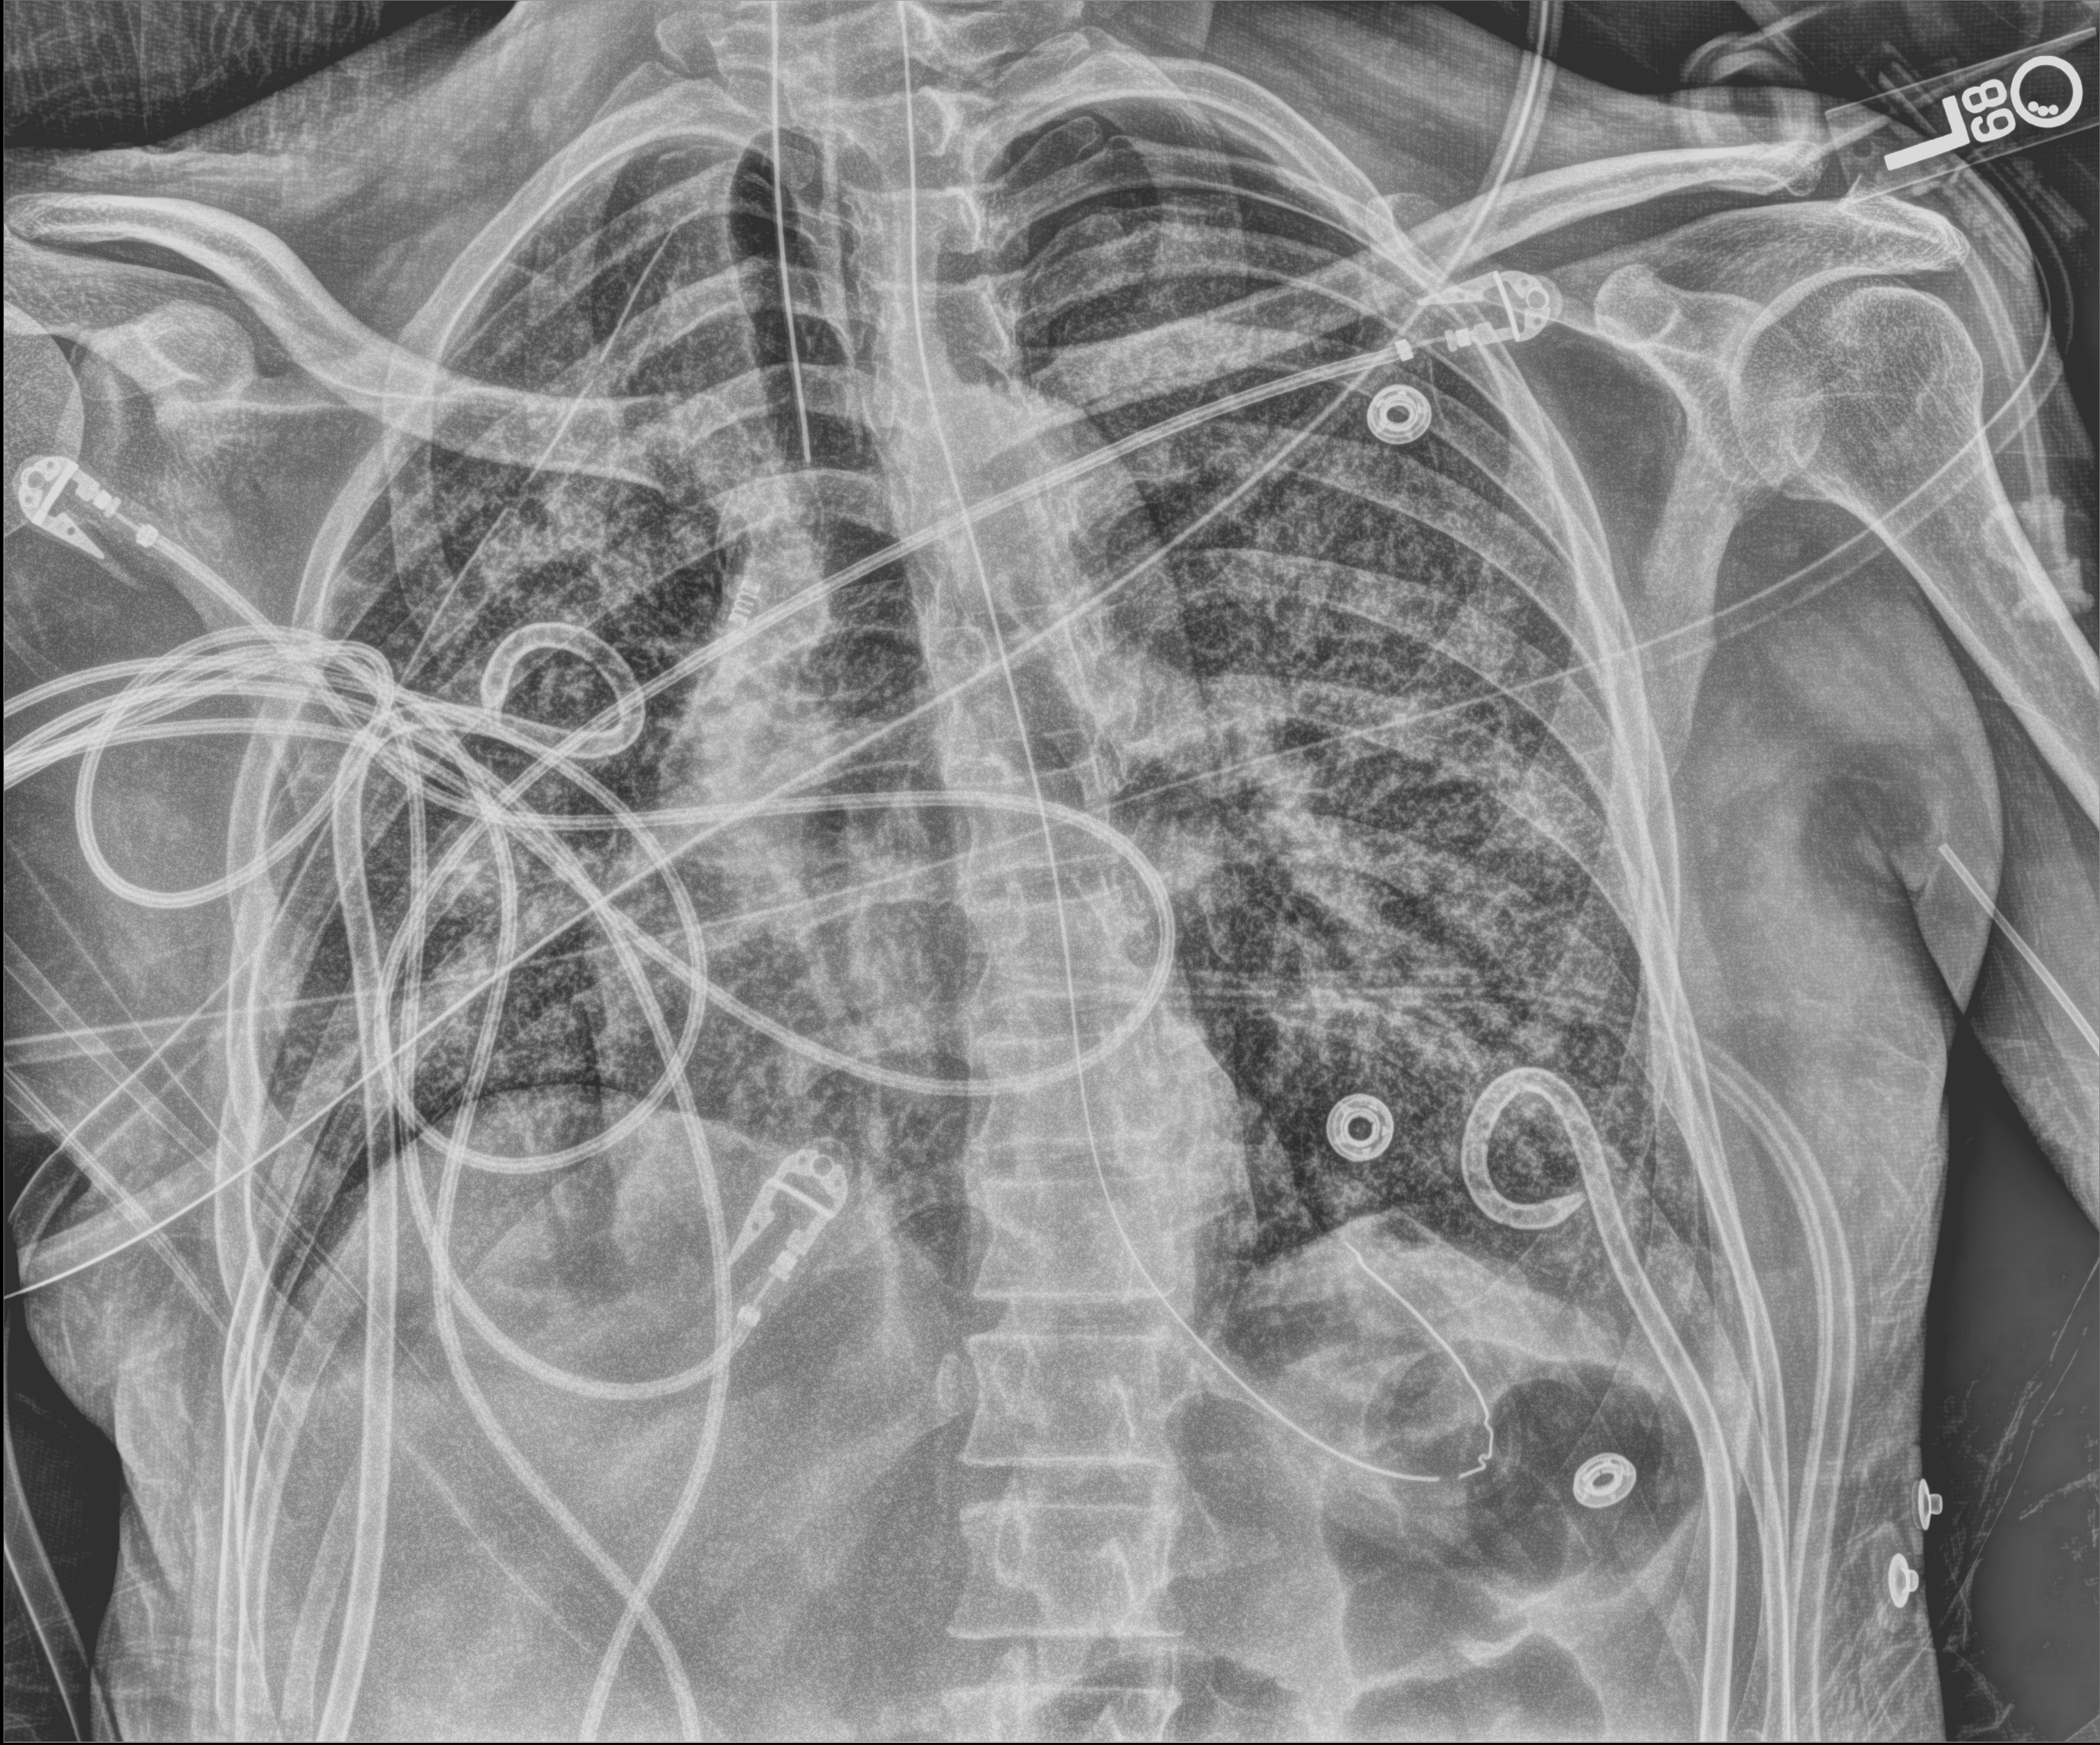
Chest X-ray (portable); anteroposterior (AP) projection. Patient hospitalised with COVID-19, aged 18–59 years.
From the hospital-stay record, not from the radiograph (when in the stay this image was taken is not recorded):
- hypertension (admission record): no
- admitted to intensive care during this hospital stay: yes
- smoking status (admission record): never